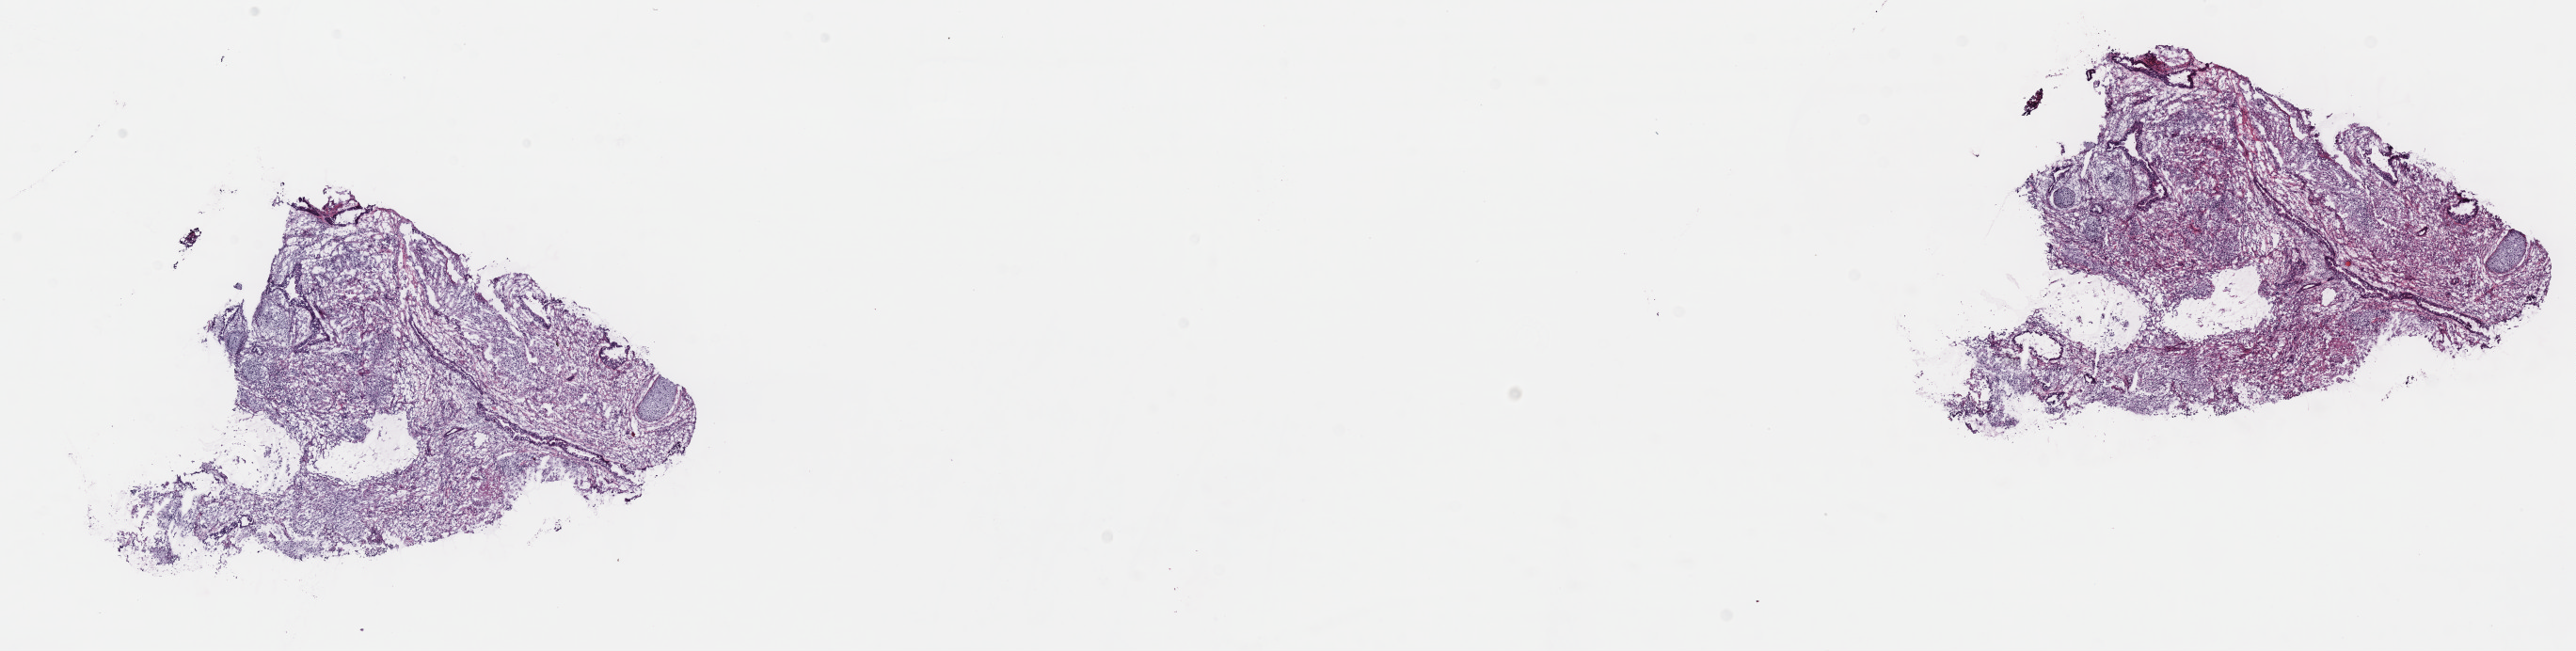
Hematoxylin and eosin (H&E) stained whole-slide image, whole scanned area (about 22.1 x 5.6 mm, slide scanned at 40x) shown as a low-resolution overview. Frozen section from the top of the tissue portion. Sample: primary tumour, testis. Patient: male, age at initial diagnosis 31 years. Slide review estimates, as recorded: tumour cells 90%, tumour nuclei 90%, normal cells 0%, stromal cells 10%, necrosis 0%. Inflammatory infiltration, as recorded: lymphocyte infiltration 5%, monocyte infiltration 0%, neutrophil infiltration 0%.
AJCC pathologic stage: IA (6th edition). Diagnosis: Teratoma, malignant, NOS. TNM: T1 NX M0.